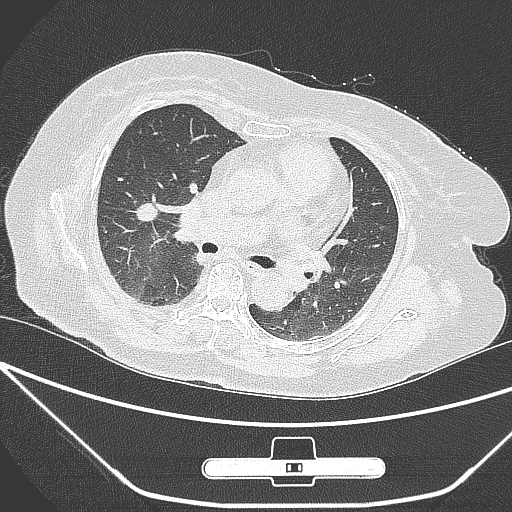
Chest CT, one axial slice. Slice 156 of 245 in the series (ordered by position). Lung window (W 1500 / L -600 HU). 512 × 512 image matrix. Patient: female, 65 years. Case-level facts recorded for this patient, not image findings: clinical TNM (as recorded): T1c N0 M0.
Structures marked on this image (bounding box drawn by a radiologist):
- lung tumour (recorded histology: adenocarcinoma): bounding box <129,192,165,235> (left, top, right, bottom; pixels)